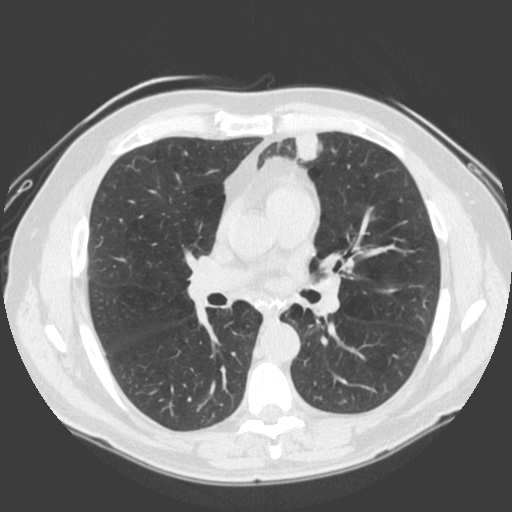
Low-dose screening chest CT, one axial slice; position 102 of 185 along the scan axis; 120 kVp; lung window (W 1500 / L -600 HU); 512 × 512 image matrix, field of view 360 × 360 mm.
Structures marked on this image (expert manual segmentation):
- lesion 1 (tumor, lower lobe of left lung): bounding box <295,133,323,162> (left, top, right, bottom; pixels)